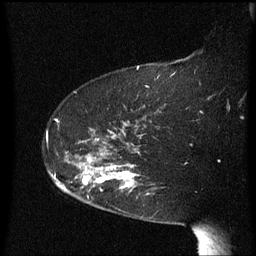
Breast MRI (dynamic contrast-enhanced), one sagittal slice; position 46 of 60 along the scan axis; dynamic contrast-enhanced series, image 2 of 3 at this slice position (ordered by acquisition); 1.5 T; TE 4.2 ms, TR 8.4 ms; 256 × 256 image matrix, field of view 200 × 200 mm. Female patient, age 63 years. Case-level facts recorded for this patient, not image findings: setting: breast cancer imaged before/during neoadjuvant chemotherapy; receptor status: HER2-positive.
Outlined on this slice (semi-automatically segmented with operator editing):
- analysis volume of interest (the breast-tissue region the enhancement analysis was run in; not a lesion): bounding box <71,144,141,207> (left, top, right, bottom; pixels)
- tumour enhancement mask (voxels above the 70 % enhancement threshold inside the analysis volume of interest): <81,158,139,189>